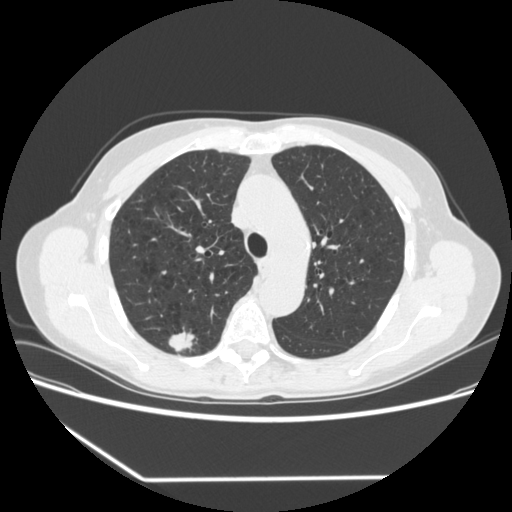
Low-dose screening chest CT, one axial slice. Slice 242 of 323 in the series (ordered by position). Reconstruction kernel STANDARD. 120 kVp. Lung window (W 1500 / L -600 HU). 512 × 512 image matrix, field of view 360 × 360 mm.
Annotated regions visible in this slice (expert manual segmentation):
- lesion 1 (tumor, upper lobe of right lung): box from (x=168, y=327) to (x=197, y=352) px